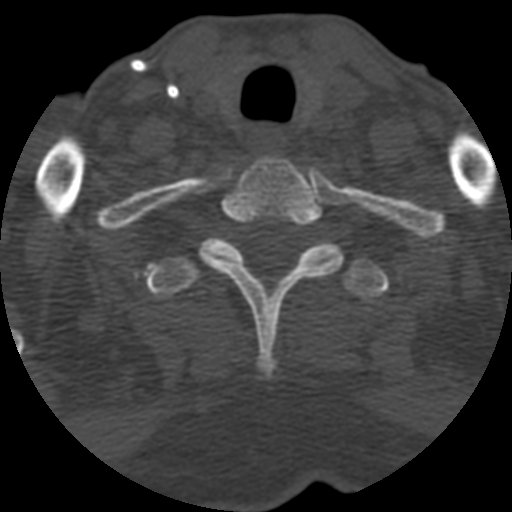
CT including the spine, one axial slice. Position 514 of 708 along the scan axis. 120 kVp. One of 3 acquisitions stored at this slice position. Bone window (W 1800 / L 400 HU). 1.25 mm slice thickness. 512 × 512 image matrix, field of view 160 × 160 mm. Patient age 55 years. From the clinical record (not read from this slice): primary cancer: colon; vertebrae with lytic lesions (as recorded): T12, L1, L5.
Outlined on this slice (semi-automatically segmented with operator editing):
- T1 vertebra: bounding box <199,156,343,370> (left, top, right, bottom; pixels)
- T2 vertebra: <144,237,390,302>